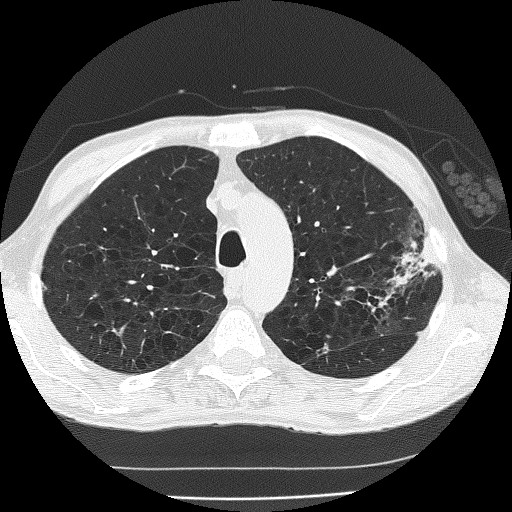
Low-dose screening chest CT, axial slice; second annual screen; lung window (W 1500 / L -600 HU); lung (sharp) reconstruction kernel (FC51); slice 46 of 185 in the series. Male, age 60 years at enrolment.
Lesion marked by an expert reader, bounding box [x1, y1, x2, y2] px = [346, 239, 443, 336]. The screening reader recorded 2 non-calcified nodules or masses ≥4 mm on this exam (left upper lobe, left upper lobe); which of them this box marks is not recorded. Official screen result: positive, other.